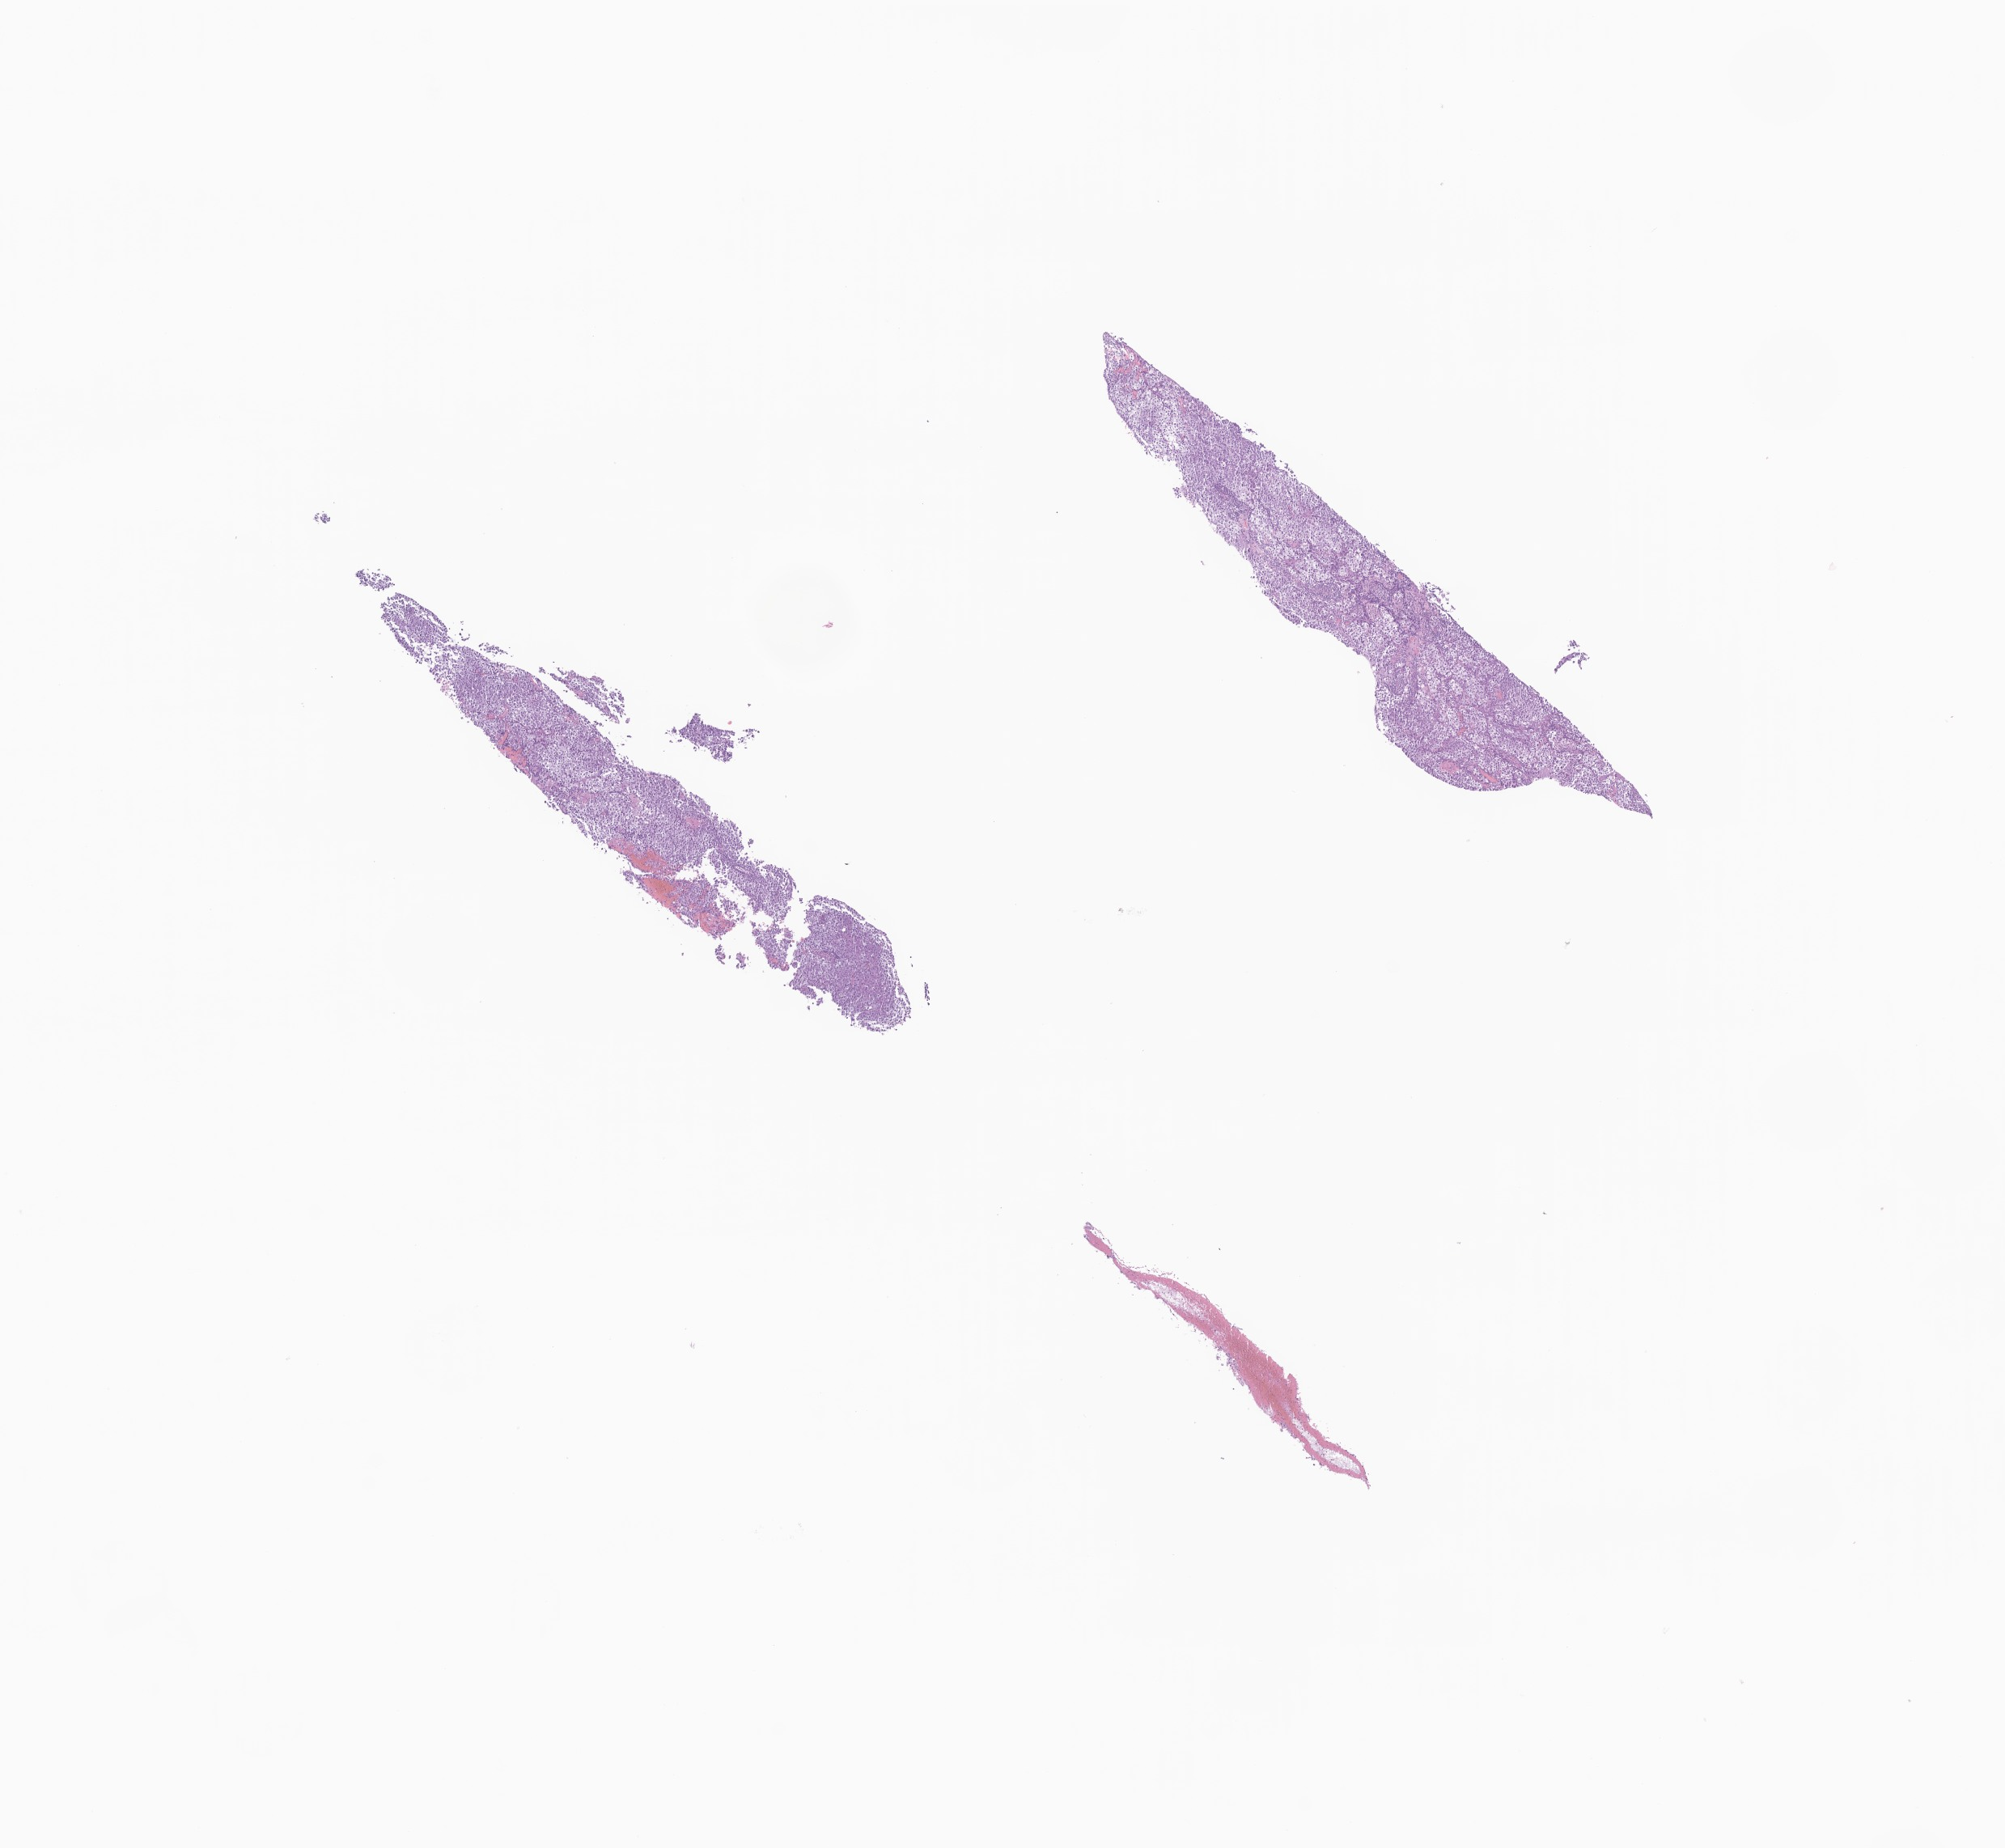
H&E whole-slide image of tumor tissue from the brain, low-resolution overview of the scanned area, about 10.4 x 9.6 mm. Formalin-fixed paraffin-embedded section. Patient: male, age 108 months (9 years).
Diagnosis: Germinoma.